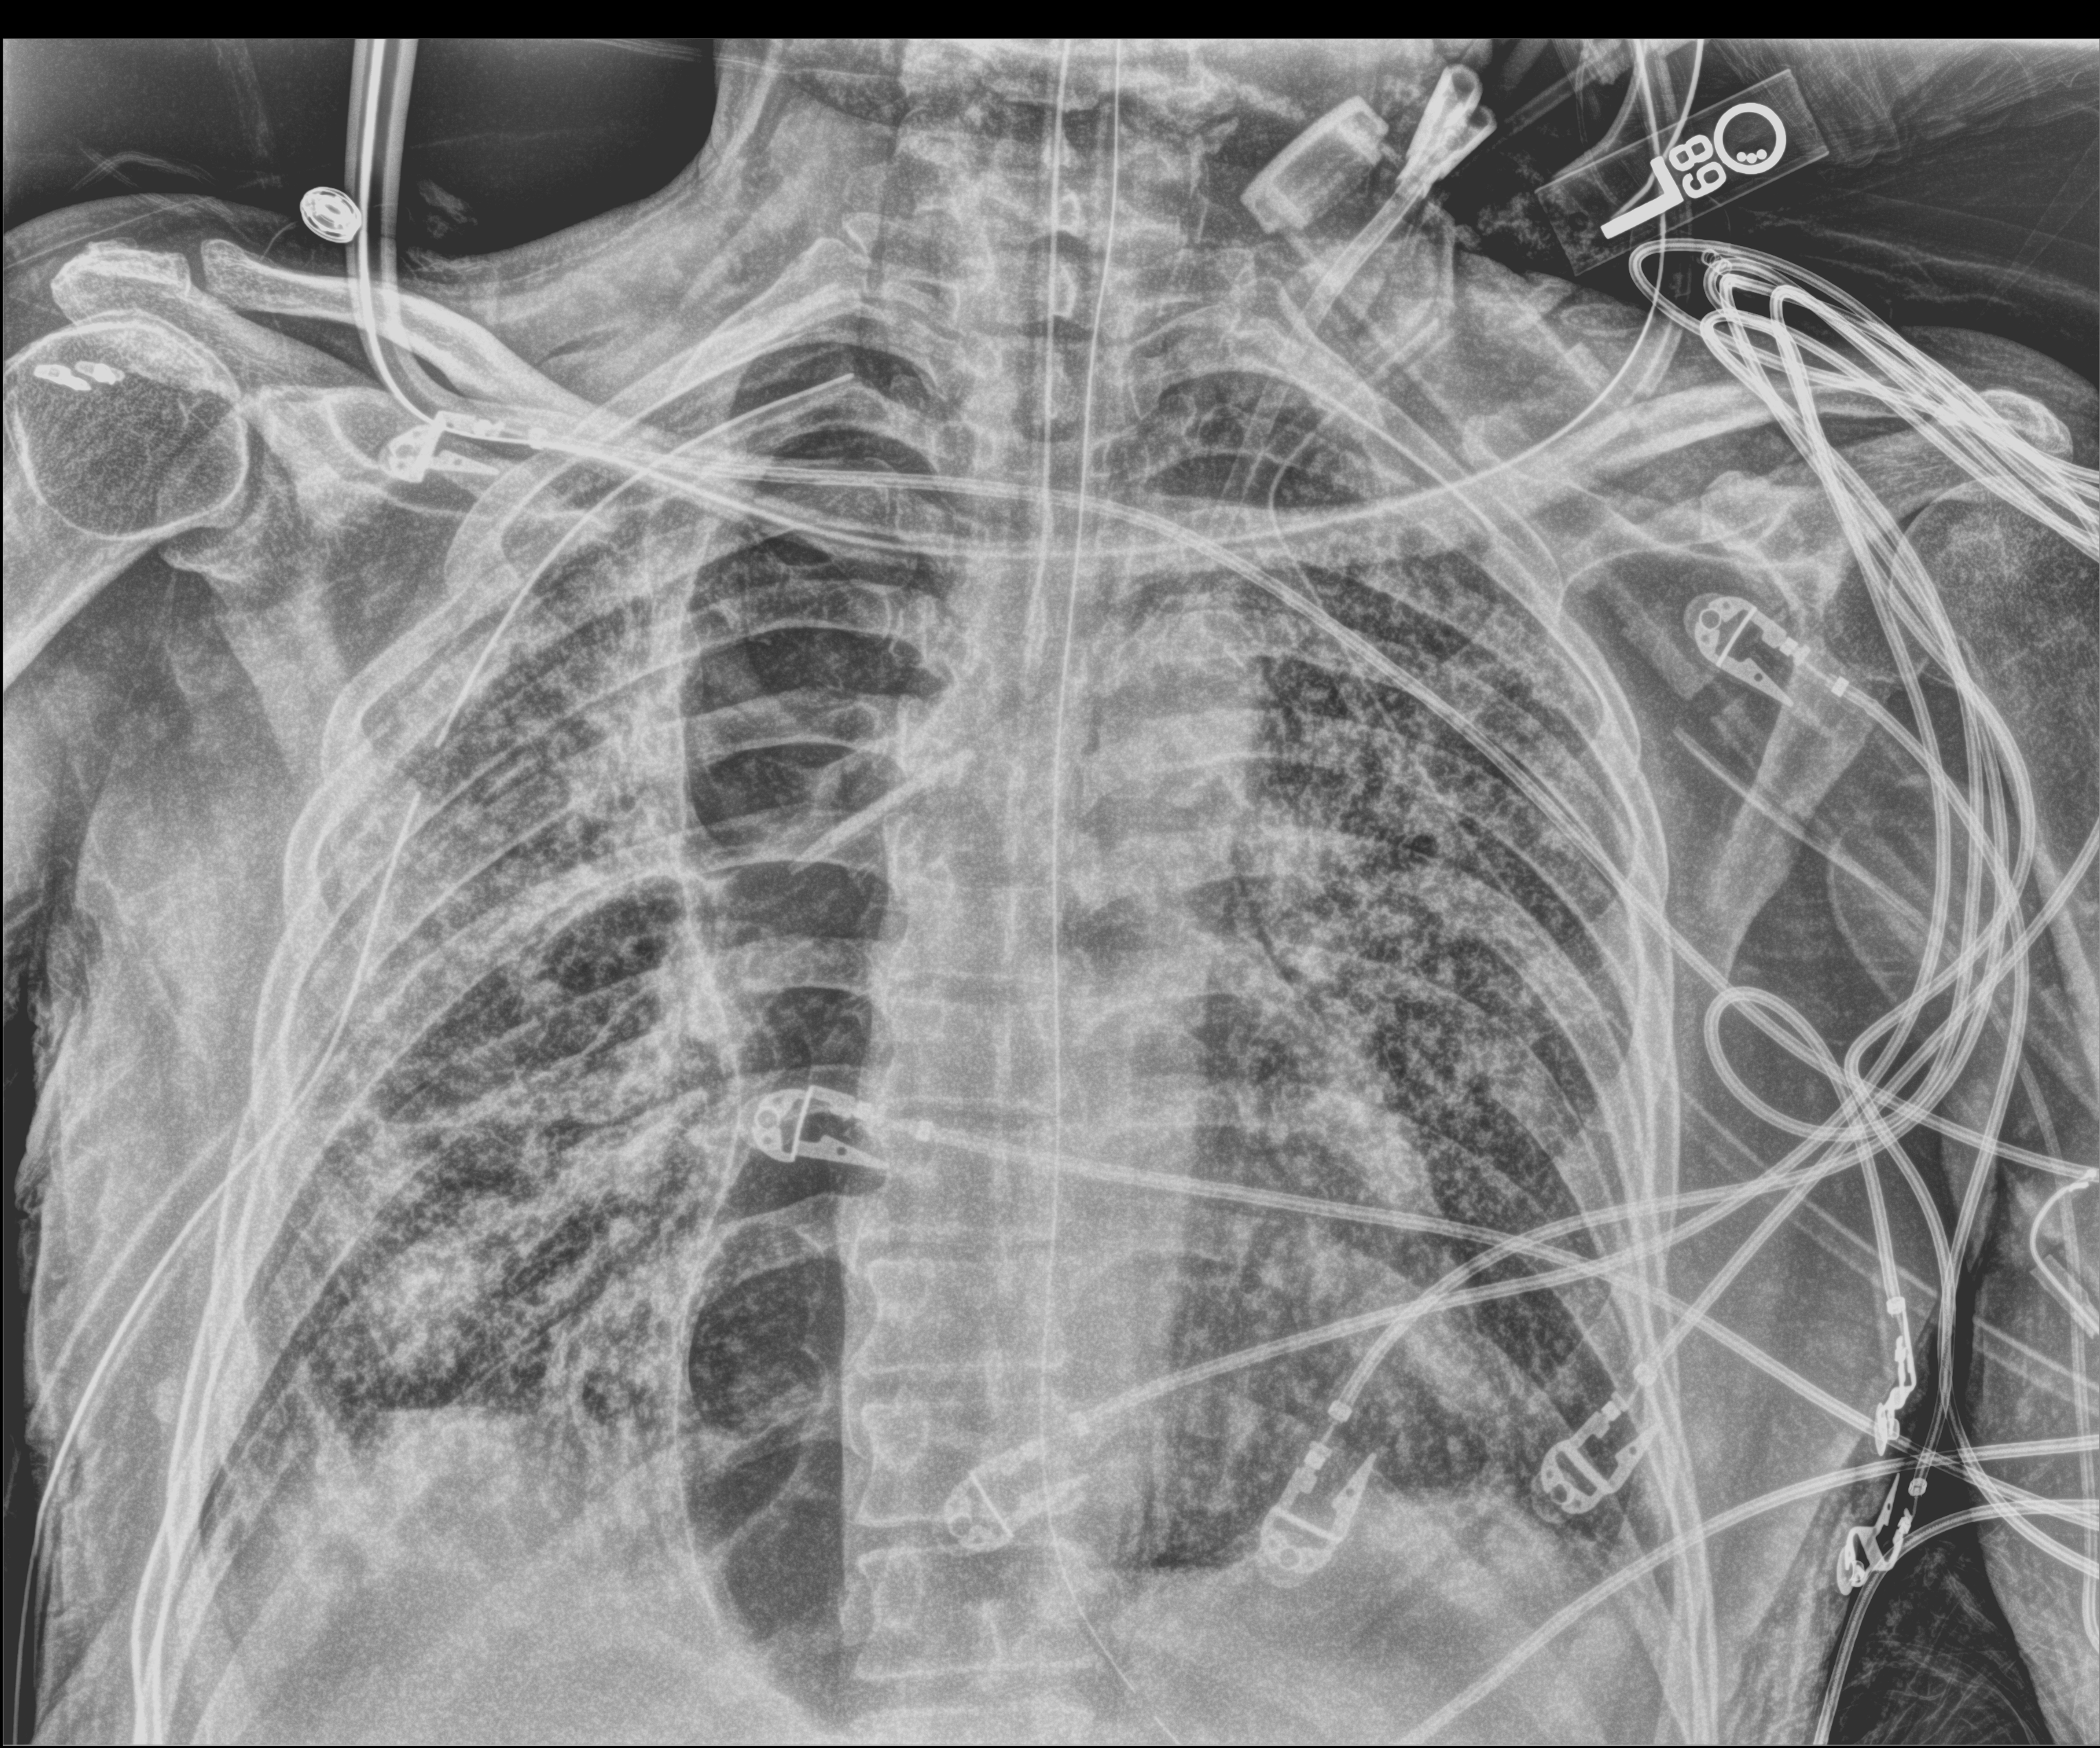
Portable chest radiograph; anteroposterior (AP) projection. Male patient hospitalised with COVID-19, age 60–74 years.
Hospital-stay facts (about this admission, not read from this image; timing relative to this image not recorded): other chronic lung disease (admission record): yes.